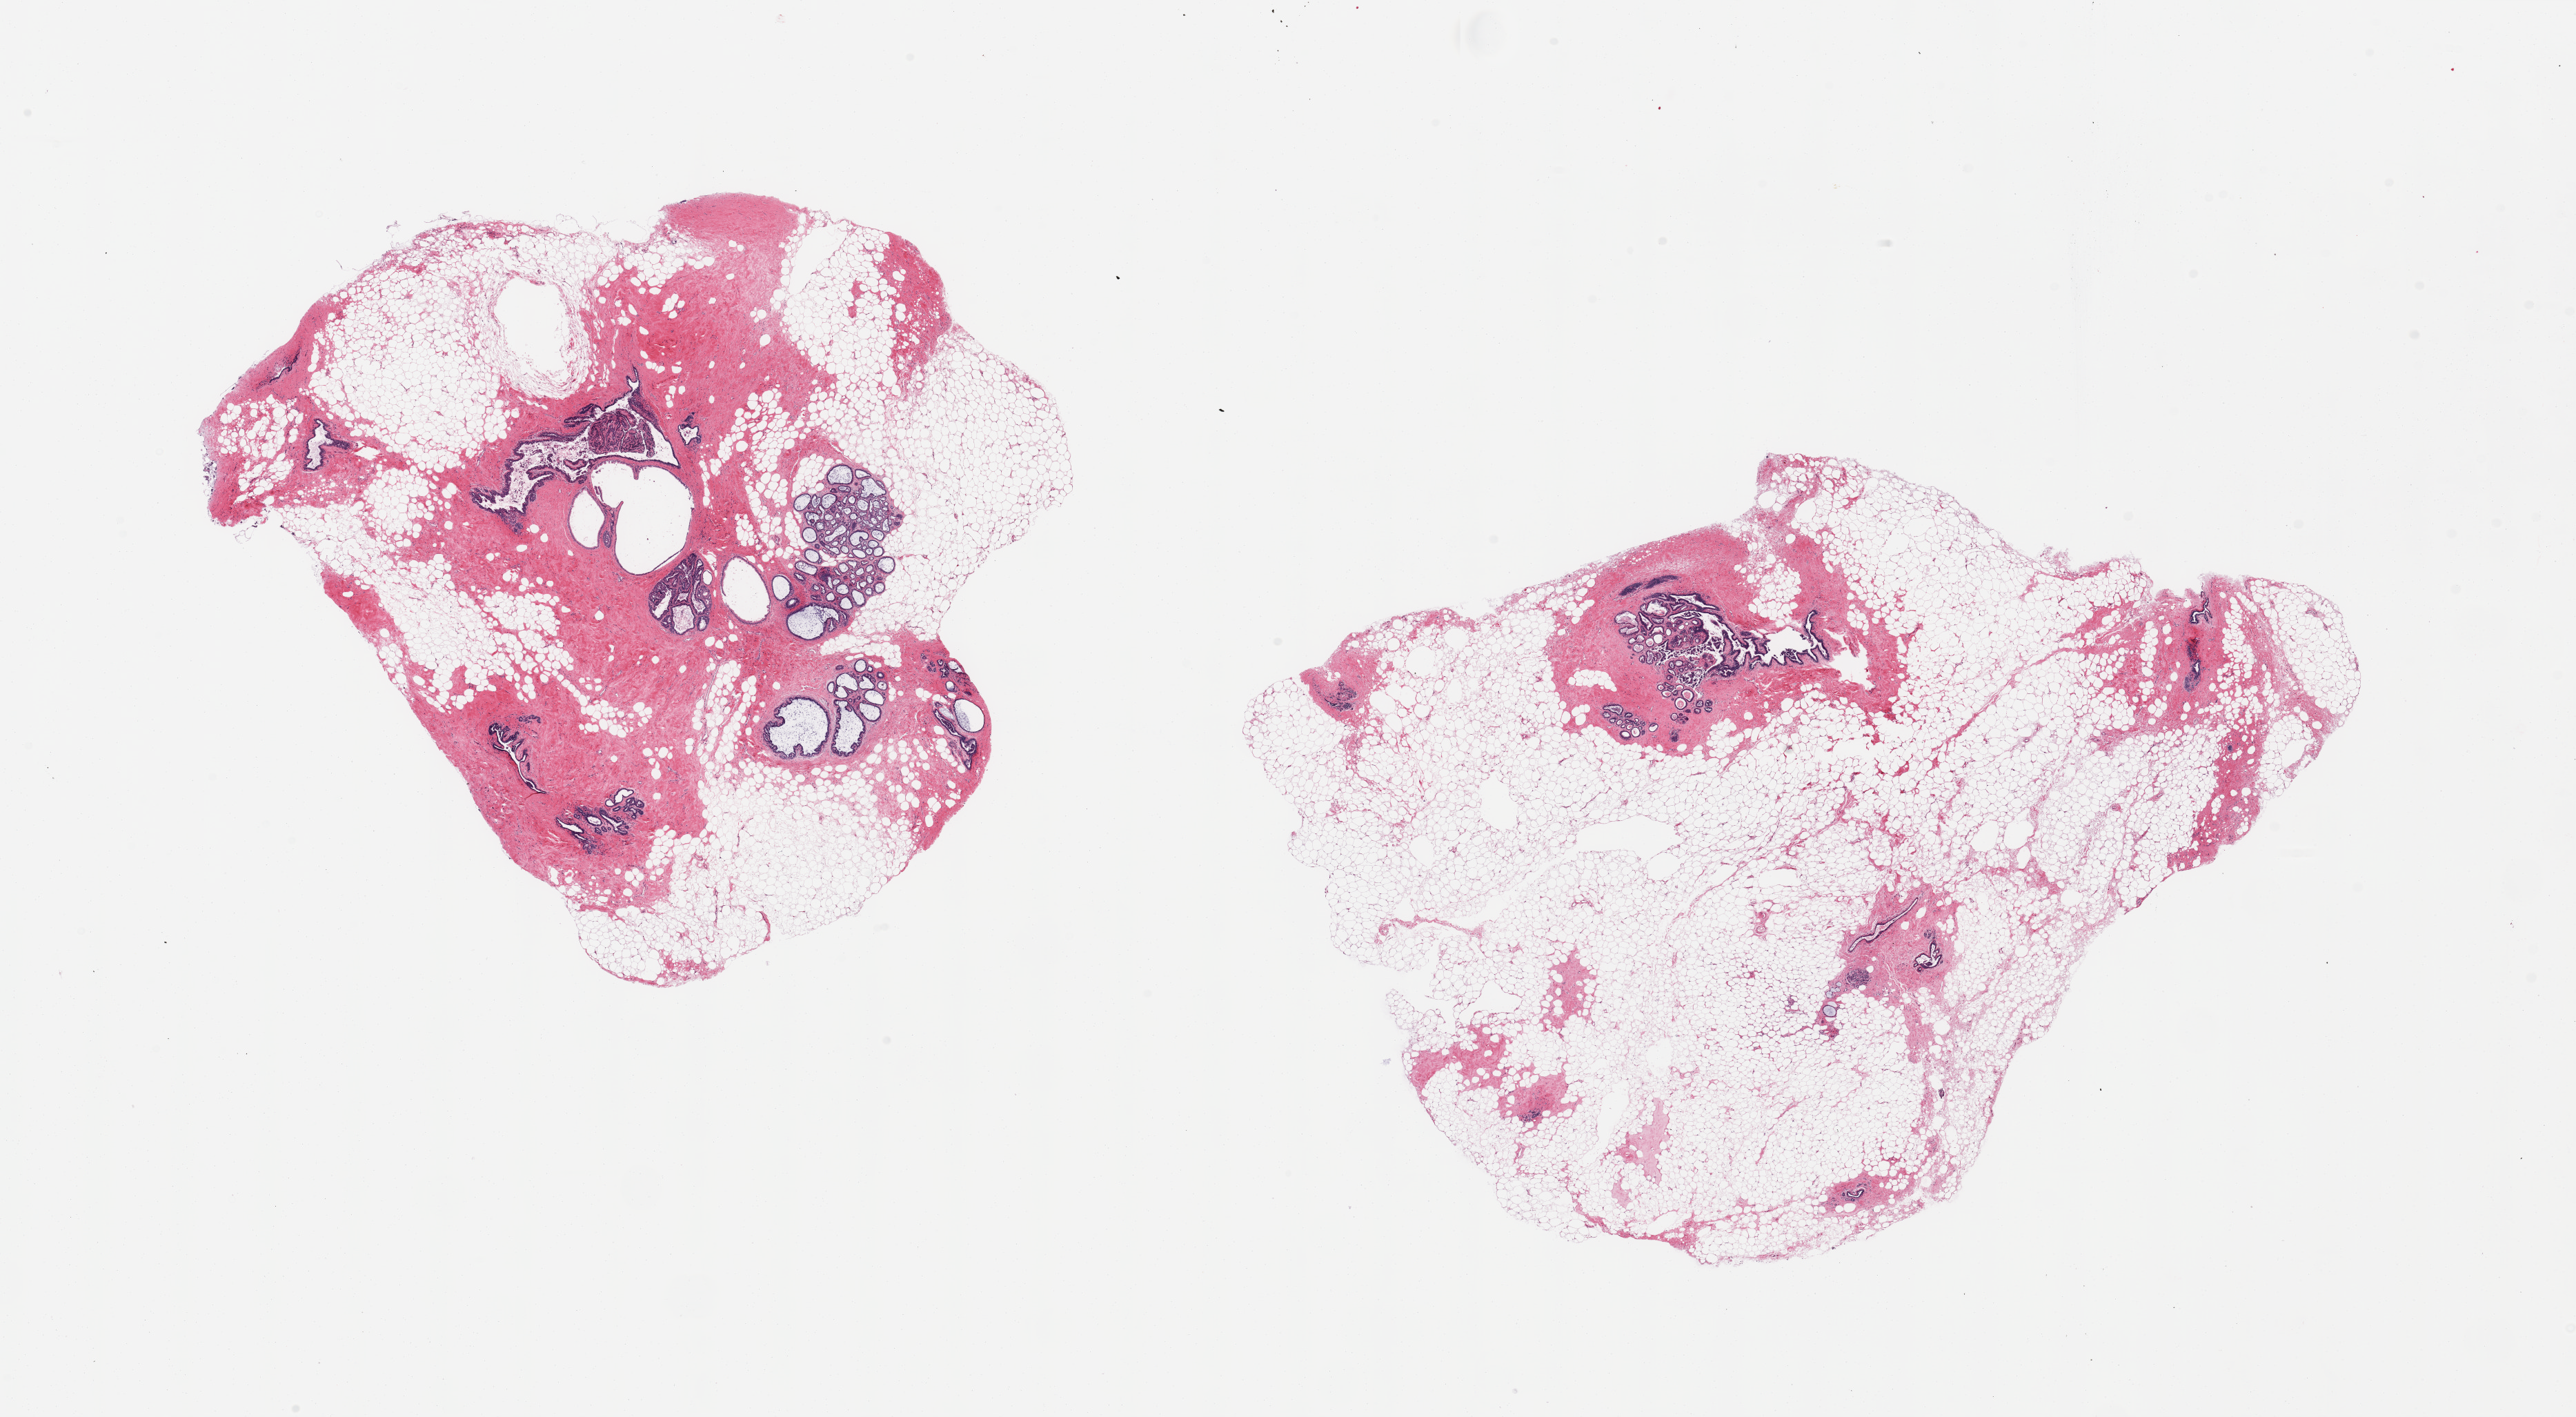
Haematoxylin and eosin whole-slide image, brightfield — a low-resolution overview of the entire scanned area, about 29.5 x 16.2 mm; PAXgene-fixed paraffin-embedded (PFPE) section; section of breast (target tissue); donor tissue sample. Donor: female.
- pathologist's review note for this sample: 2 pieces prominent fibrocystic changes/adenosis